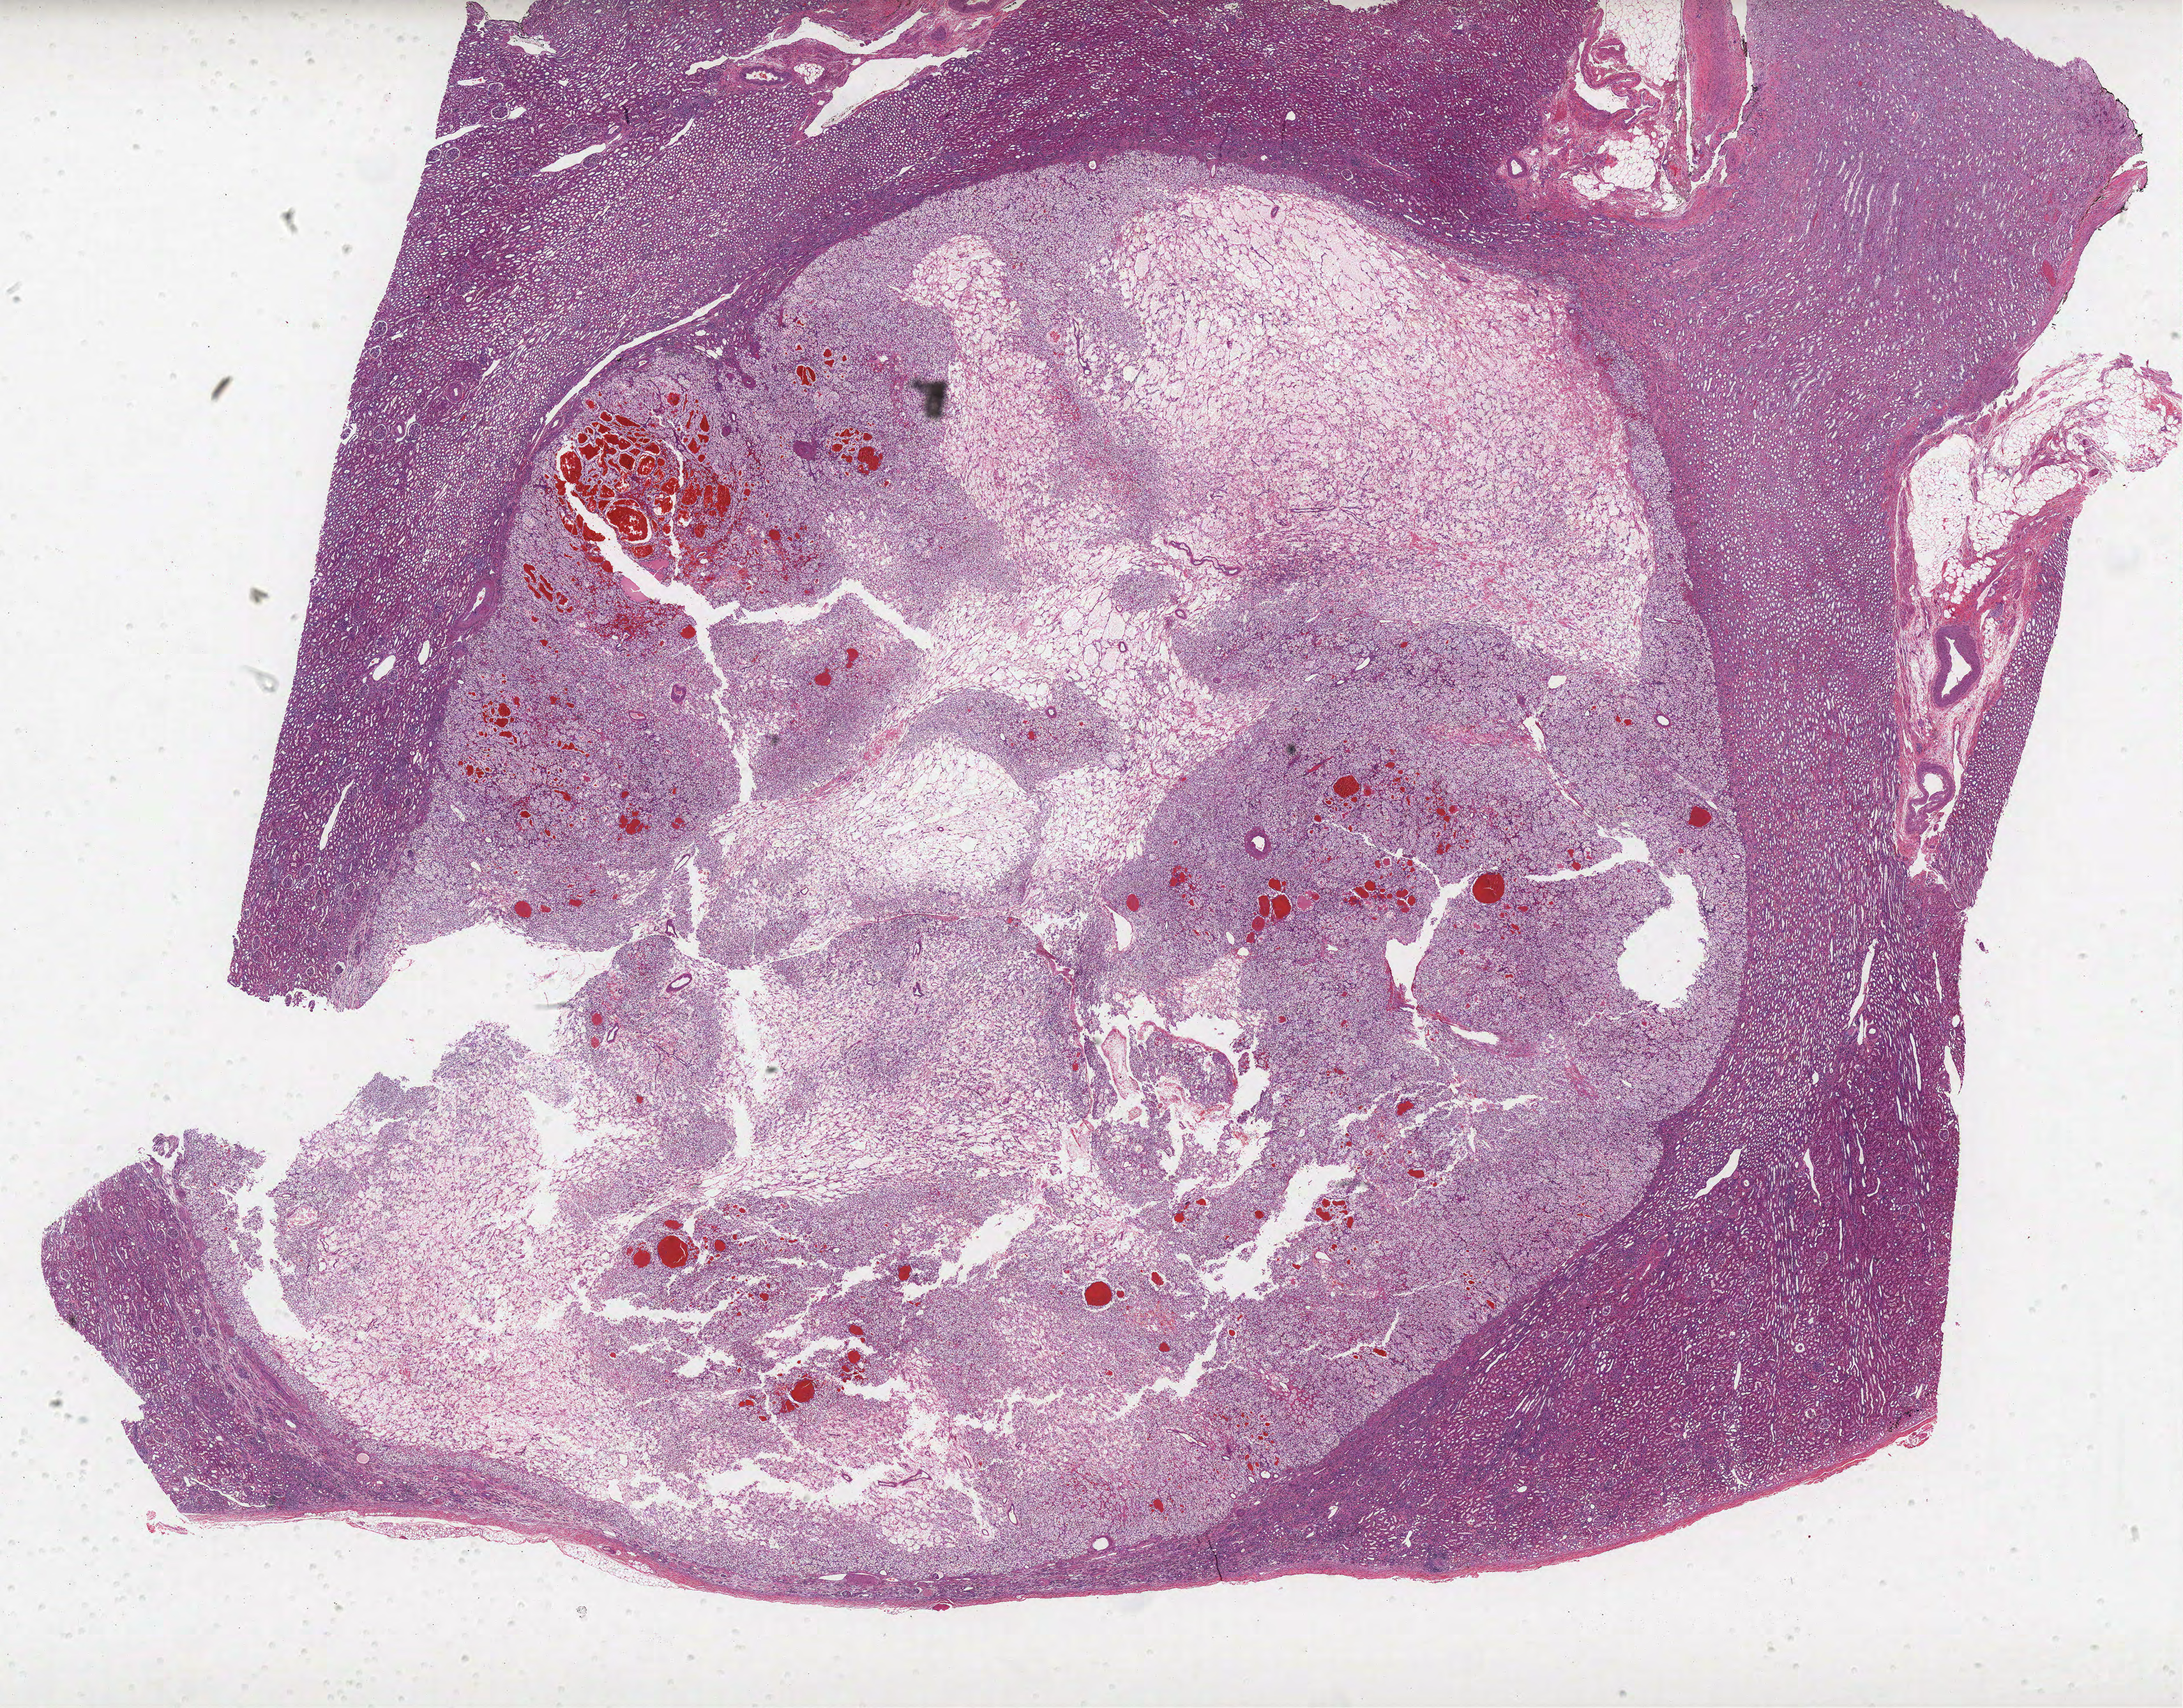
Digitized H&E-stained tissue section (whole slide) — low-resolution overview of the scanned area, about 27.3 x 21.4 mm (slide scanned at 40x), formalin-fixed paraffin-embedded (FFPE) diagnostic section, kidney, primary tumour sample. Patient: female, age at initial diagnosis 50 years.
Pathologic diagnosis: Clear cell adenocarcinoma, NOS.